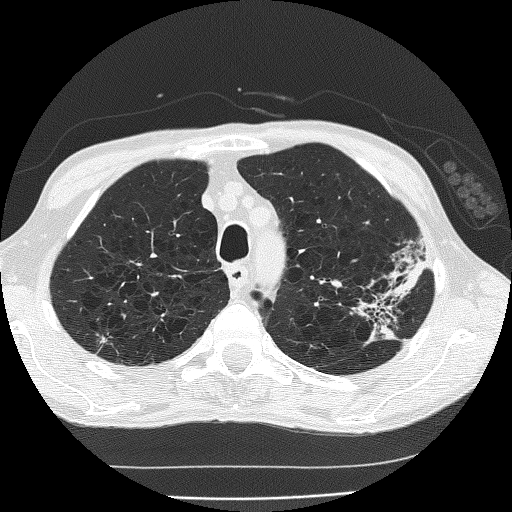
Low-dose screening chest CT, axial slice; second screening round (one year after baseline); lung window (W 1500 / L -600 HU); 2 mm slice thickness; lung (sharp) reconstruction kernel (FC51); 512 × 512 image matrix. Male participant, aged 60 years at enrolment.
- Expert reader's lesion annotation, bounding box [x1, y1, x2, y2] px = [346, 254, 433, 339].
- The screening reader recorded 2 non-calcified nodules or masses ≥4 mm on this exam (left upper lobe, left upper lobe); which of them this box marks is not recorded.
- Lung cancer was diagnosed 178 days after this screen: bronchiolo-alveolar carcinoma, mucinous, left upper lobe, stage IV (AJCC 6th edition).